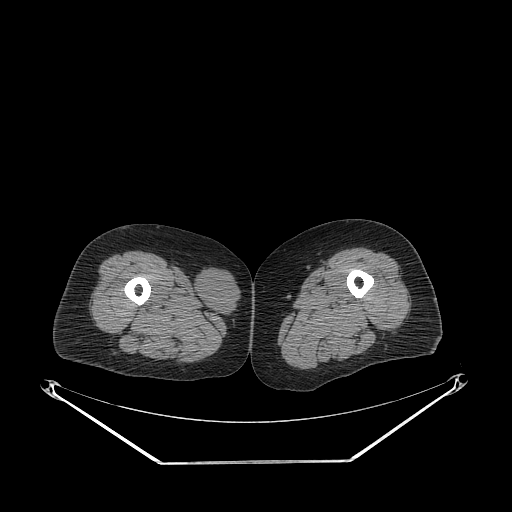
CT of an extremity soft-tissue mass (from a PET/CT study), one axial slice. Slice 236 of 311 in the series (ordered by position). Reconstruction kernel STANDARD. Soft-tissue window (W 400 / L 40 HU). 512 × 512 image matrix, field of view 500 × 500 mm. Female patient. From the clinical record (not read from this slice): histological type: leiomyosarcoma; grade: intermediate; site of the primary tumour: parascapusular.
Annotated regions visible in this slice (expert contour drawn on MRI and transferred to this co-registered scan by the dataset authors):
- gross tumour volume including surrounding oedema: bounding box (x1, y1, x2, y2) in pixels: (194, 267, 241, 318)
- gross tumour volume (mass): (194, 267, 241, 318)